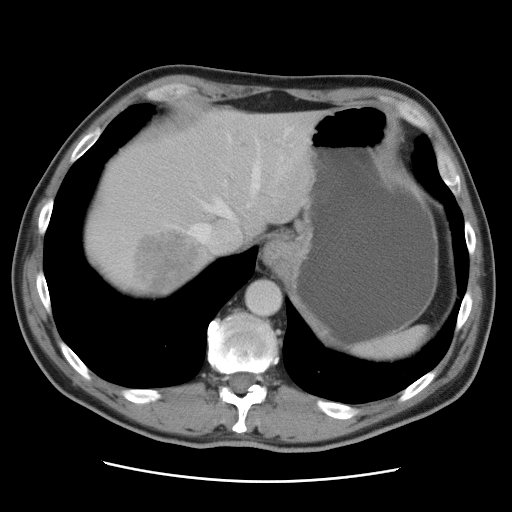
Contrast-enhanced abdominal CT, one axial slice. Slice 75 of 89 in the series (ordered by position). Intravenous contrast given. Soft-tissue window (W 400 / L 40 HU). 5 mm slice thickness. 512 × 512 image matrix, field of view 366 × 366 mm. Male patient, age 59 years. From the clinical record (not read from this slice): diagnosis: colorectal cancer liver metastases, imaged before liver resection; multiple liver metastases: yes; largest metastasis: 0.6 cm; disease in both lobes: yes.
Outlined on this slice (outlined manually by an expert reader):
- hepatic veins: bounding box <189,127,291,256> (left, top, right, bottom; pixels)
- liver: <84,109,320,298>
- planned liver remnant (the part of the liver to remain after resection): <127,109,323,243>
- liver metastasis: <137,234,206,294>